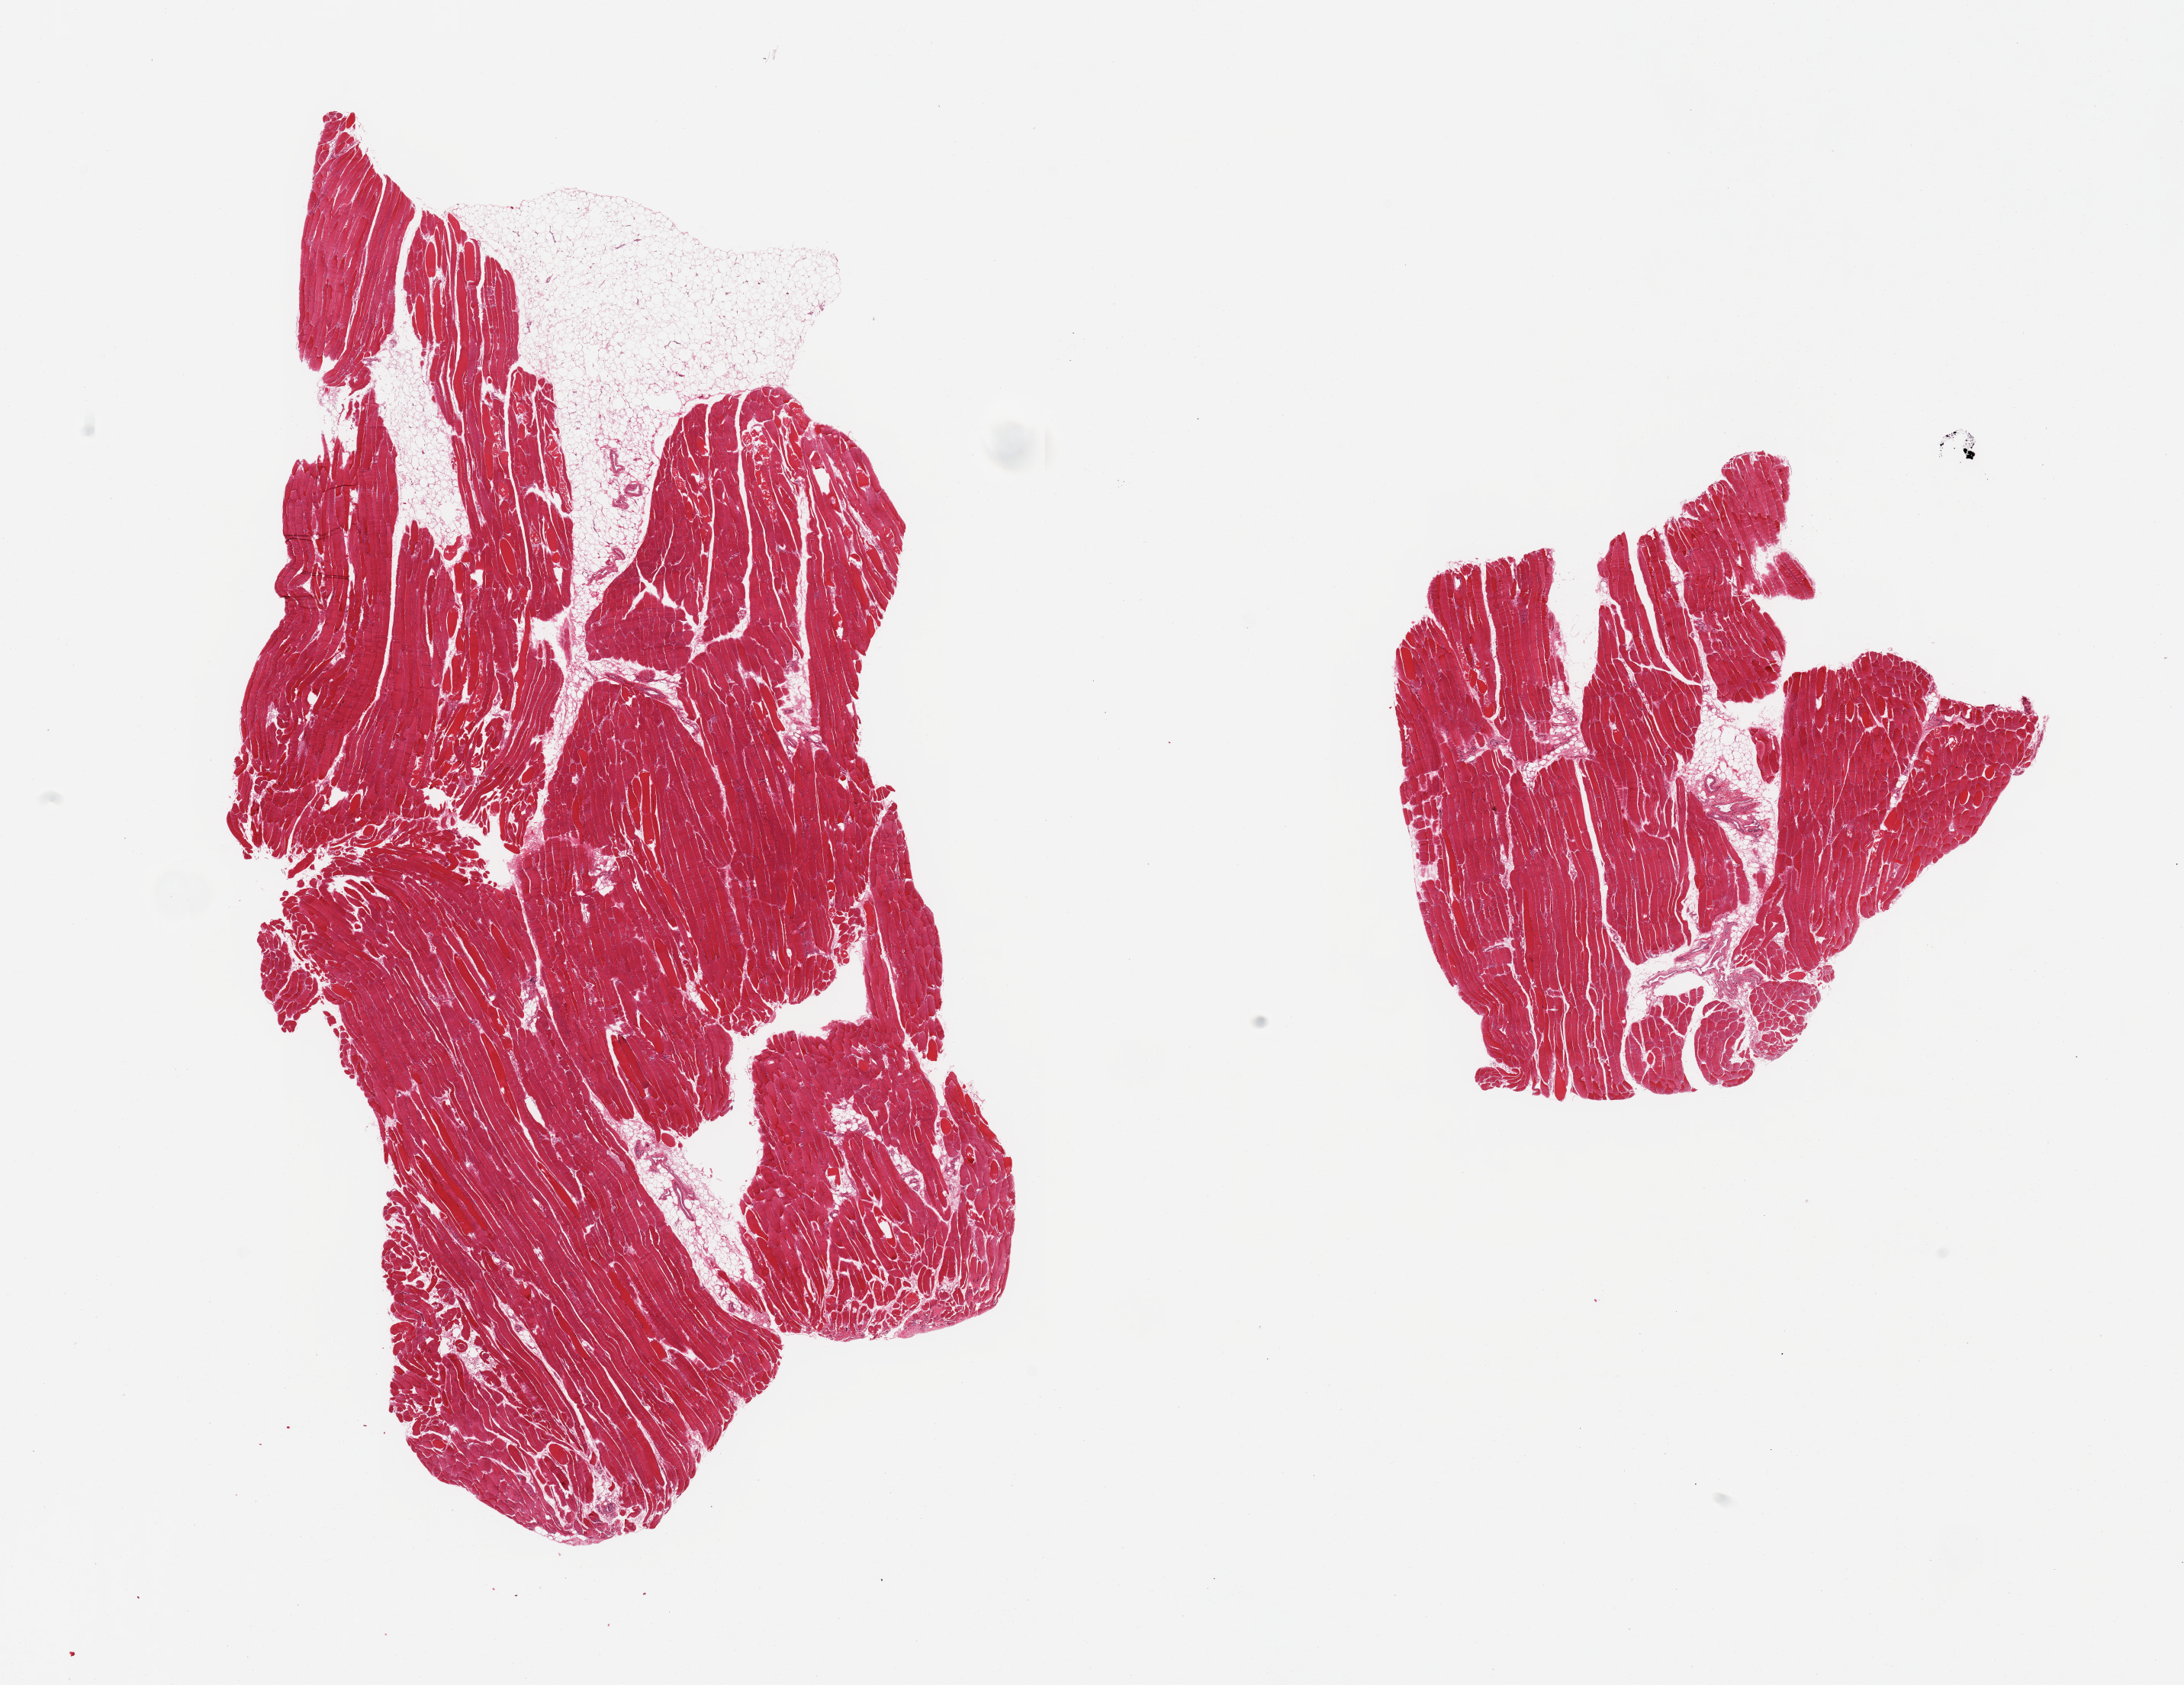
Digitized haematoxylin and eosin-stained section — whole scanned area (about 22.6 x 17.5 mm) shown as a low-resolution overview; PAXgene-fixed paraffin-embedded (PFPE) section; section of skeletal muscle (target tissue); tissue donor sample. Donor: female.
* review note (as recorded): 2 pieces; 1 piece includes ~10% attached fat